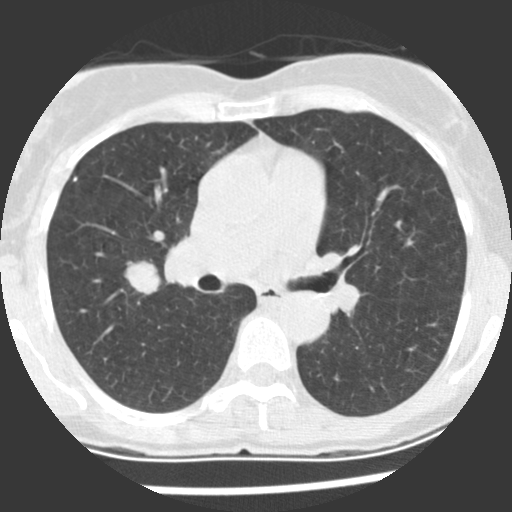
Low-dose screening chest CT, axial slice, baseline annual screen, lung window (W 1500 / L -600 HU), standard (soft-tissue) reconstruction kernel (STANDARD), slice 100 of 225 in the series. Female, age 60 years at enrolment. Current smoker at enrolment.
Lesion marked by an expert reader, bounding box (x1, y1, x2, y2) in pixels: (115, 255, 172, 301). The screening reader recorded 2 non-calcified nodules or masses ≥4 mm on this exam (right upper lobe, right middle lobe); which of them this box marks is not recorded. Official screen result: positive, change unspecified: nodule(s) >= 4 mm or enlarging nodule(s), mass(es), or other non-specific abnormalities suspicious for lung cancer.